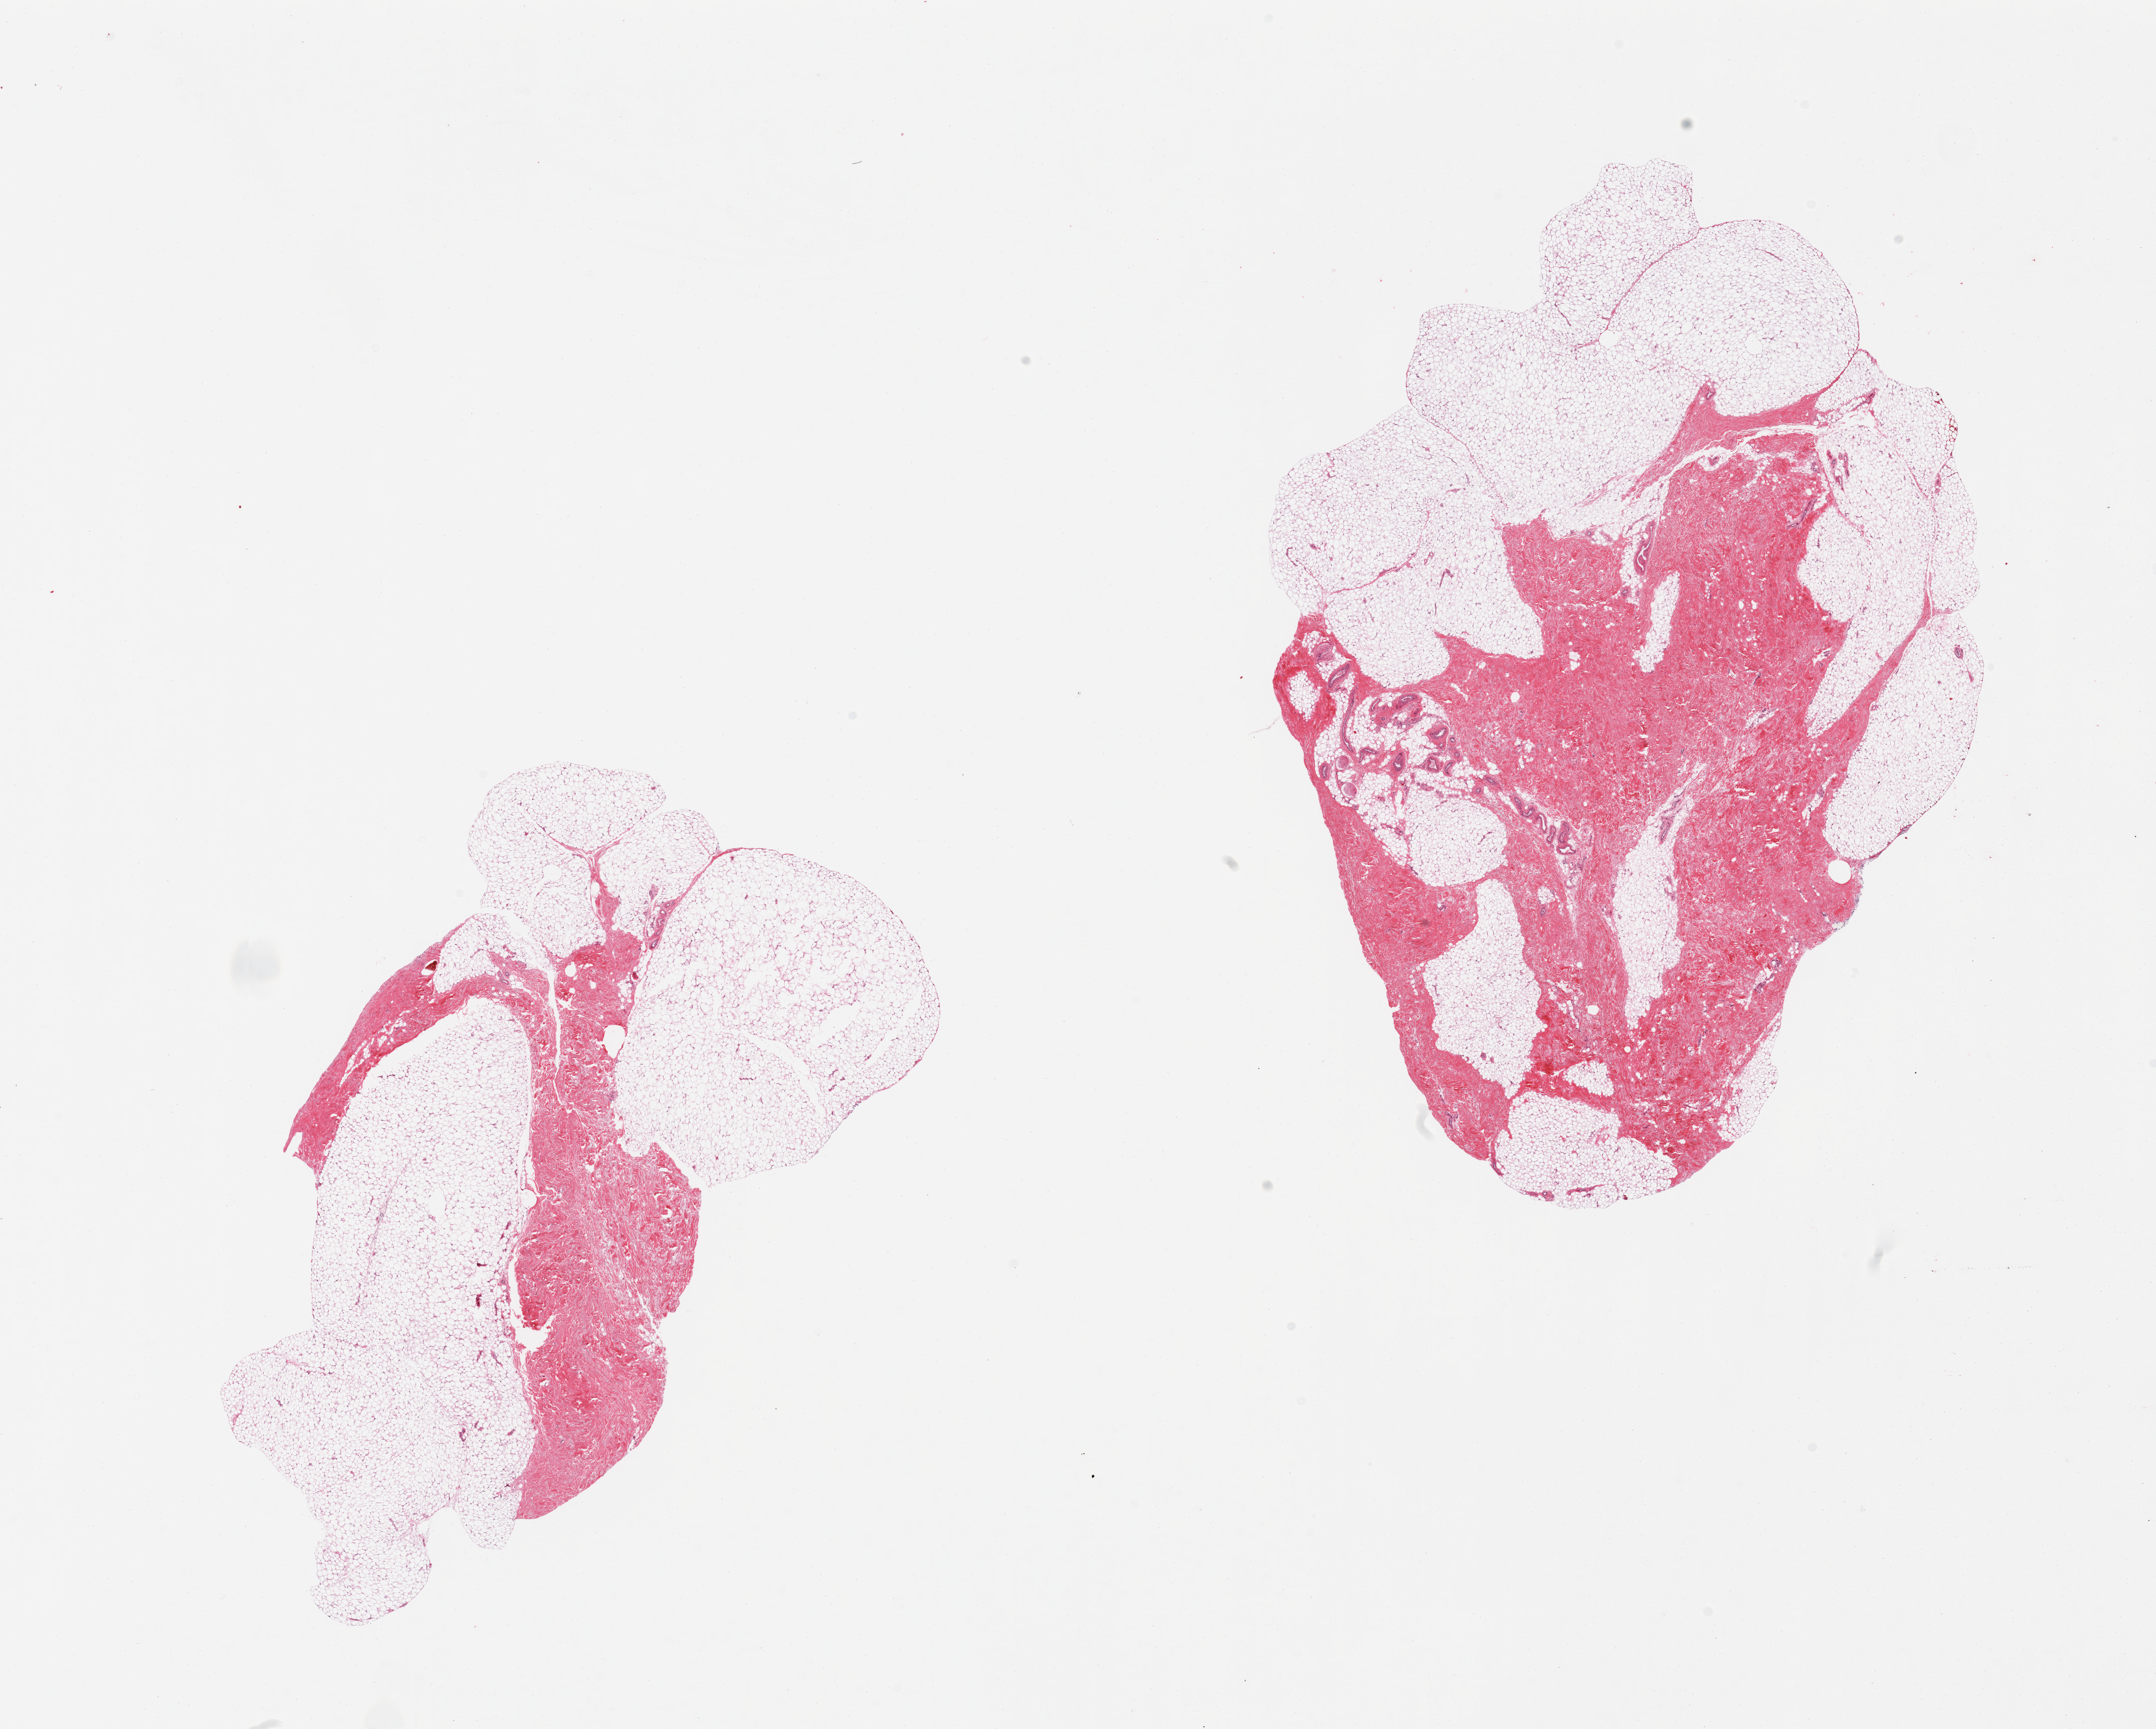
Whole-slide image, H&E stain, brightfield, shown as a low-resolution overview of the whole scanned area (about 25.6 x 20.5 mm, slide scanned at 20x). PAXgene-fixed paraffin-embedded (PFPE) section. Target tissue: breast. Tissue donor sample. Male donor.
• review note (as recorded): 2 pieces, 30 and 50% fibrous tissue, no appreciable ducts/lobules